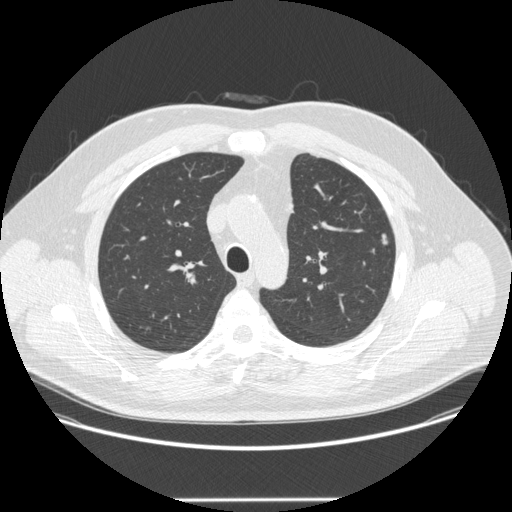
Chest CT (low-dose screening protocol), one axial image; first (baseline) screen; lung window (W 1500 / L -600 HU); 120 kVp; slice 66 of 252 in the series. Male participant, aged 55 years at enrolment. Former smoker at enrolment.
Expert reader's lesion annotation, bounding box [x1, y1, x2, y2] px = [373, 229, 402, 255]. The exam's reader record, not a measurement of the box and not confirmed to be the same lesion: non-calcified nodule or mass ≥4 mm, left upper lobe, 5 × 4 mm, smooth margins, soft tissue attenuation. Lung cancer was diagnosed 462 days after this screen: adenocarcinoma, NOS, left upper lobe, moderately differentiated (G2), stage IA (AJCC 6th edition), 9 mm at pathology.